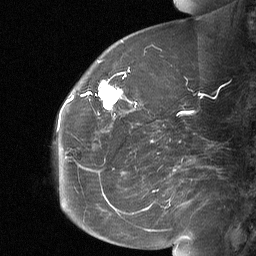
Breast MRI (dynamic contrast-enhanced), one sagittal slice. Slice 22 of 64 in the series (ordered by position). Dynamic contrast-enhanced study with each time point stored as its own series, time point 2 of 3 at this slice position (early post-contrast, ordered by acquisition time). 1.5 T. TE 4.8 ms, TR 27 ms. 2 mm slice thickness. 256 × 256 image matrix. Female patient, age 60 years. From the clinical record (not read from this slice): setting: breast cancer imaged before/during neoadjuvant chemotherapy; receptor status: HR-positive, HER2-negative.
Annotated regions visible in this slice (semi-automatic segmentation, software-assisted and operator-edited):
- analysis volume of interest (the breast-tissue region the enhancement analysis was run in; not a lesion): box from (x=92, y=70) to (x=134, y=112) px
- tumour enhancement mask (voxels above the 90 % enhancement threshold inside the analysis volume of interest): (x=98, y=71)–(x=130, y=110)